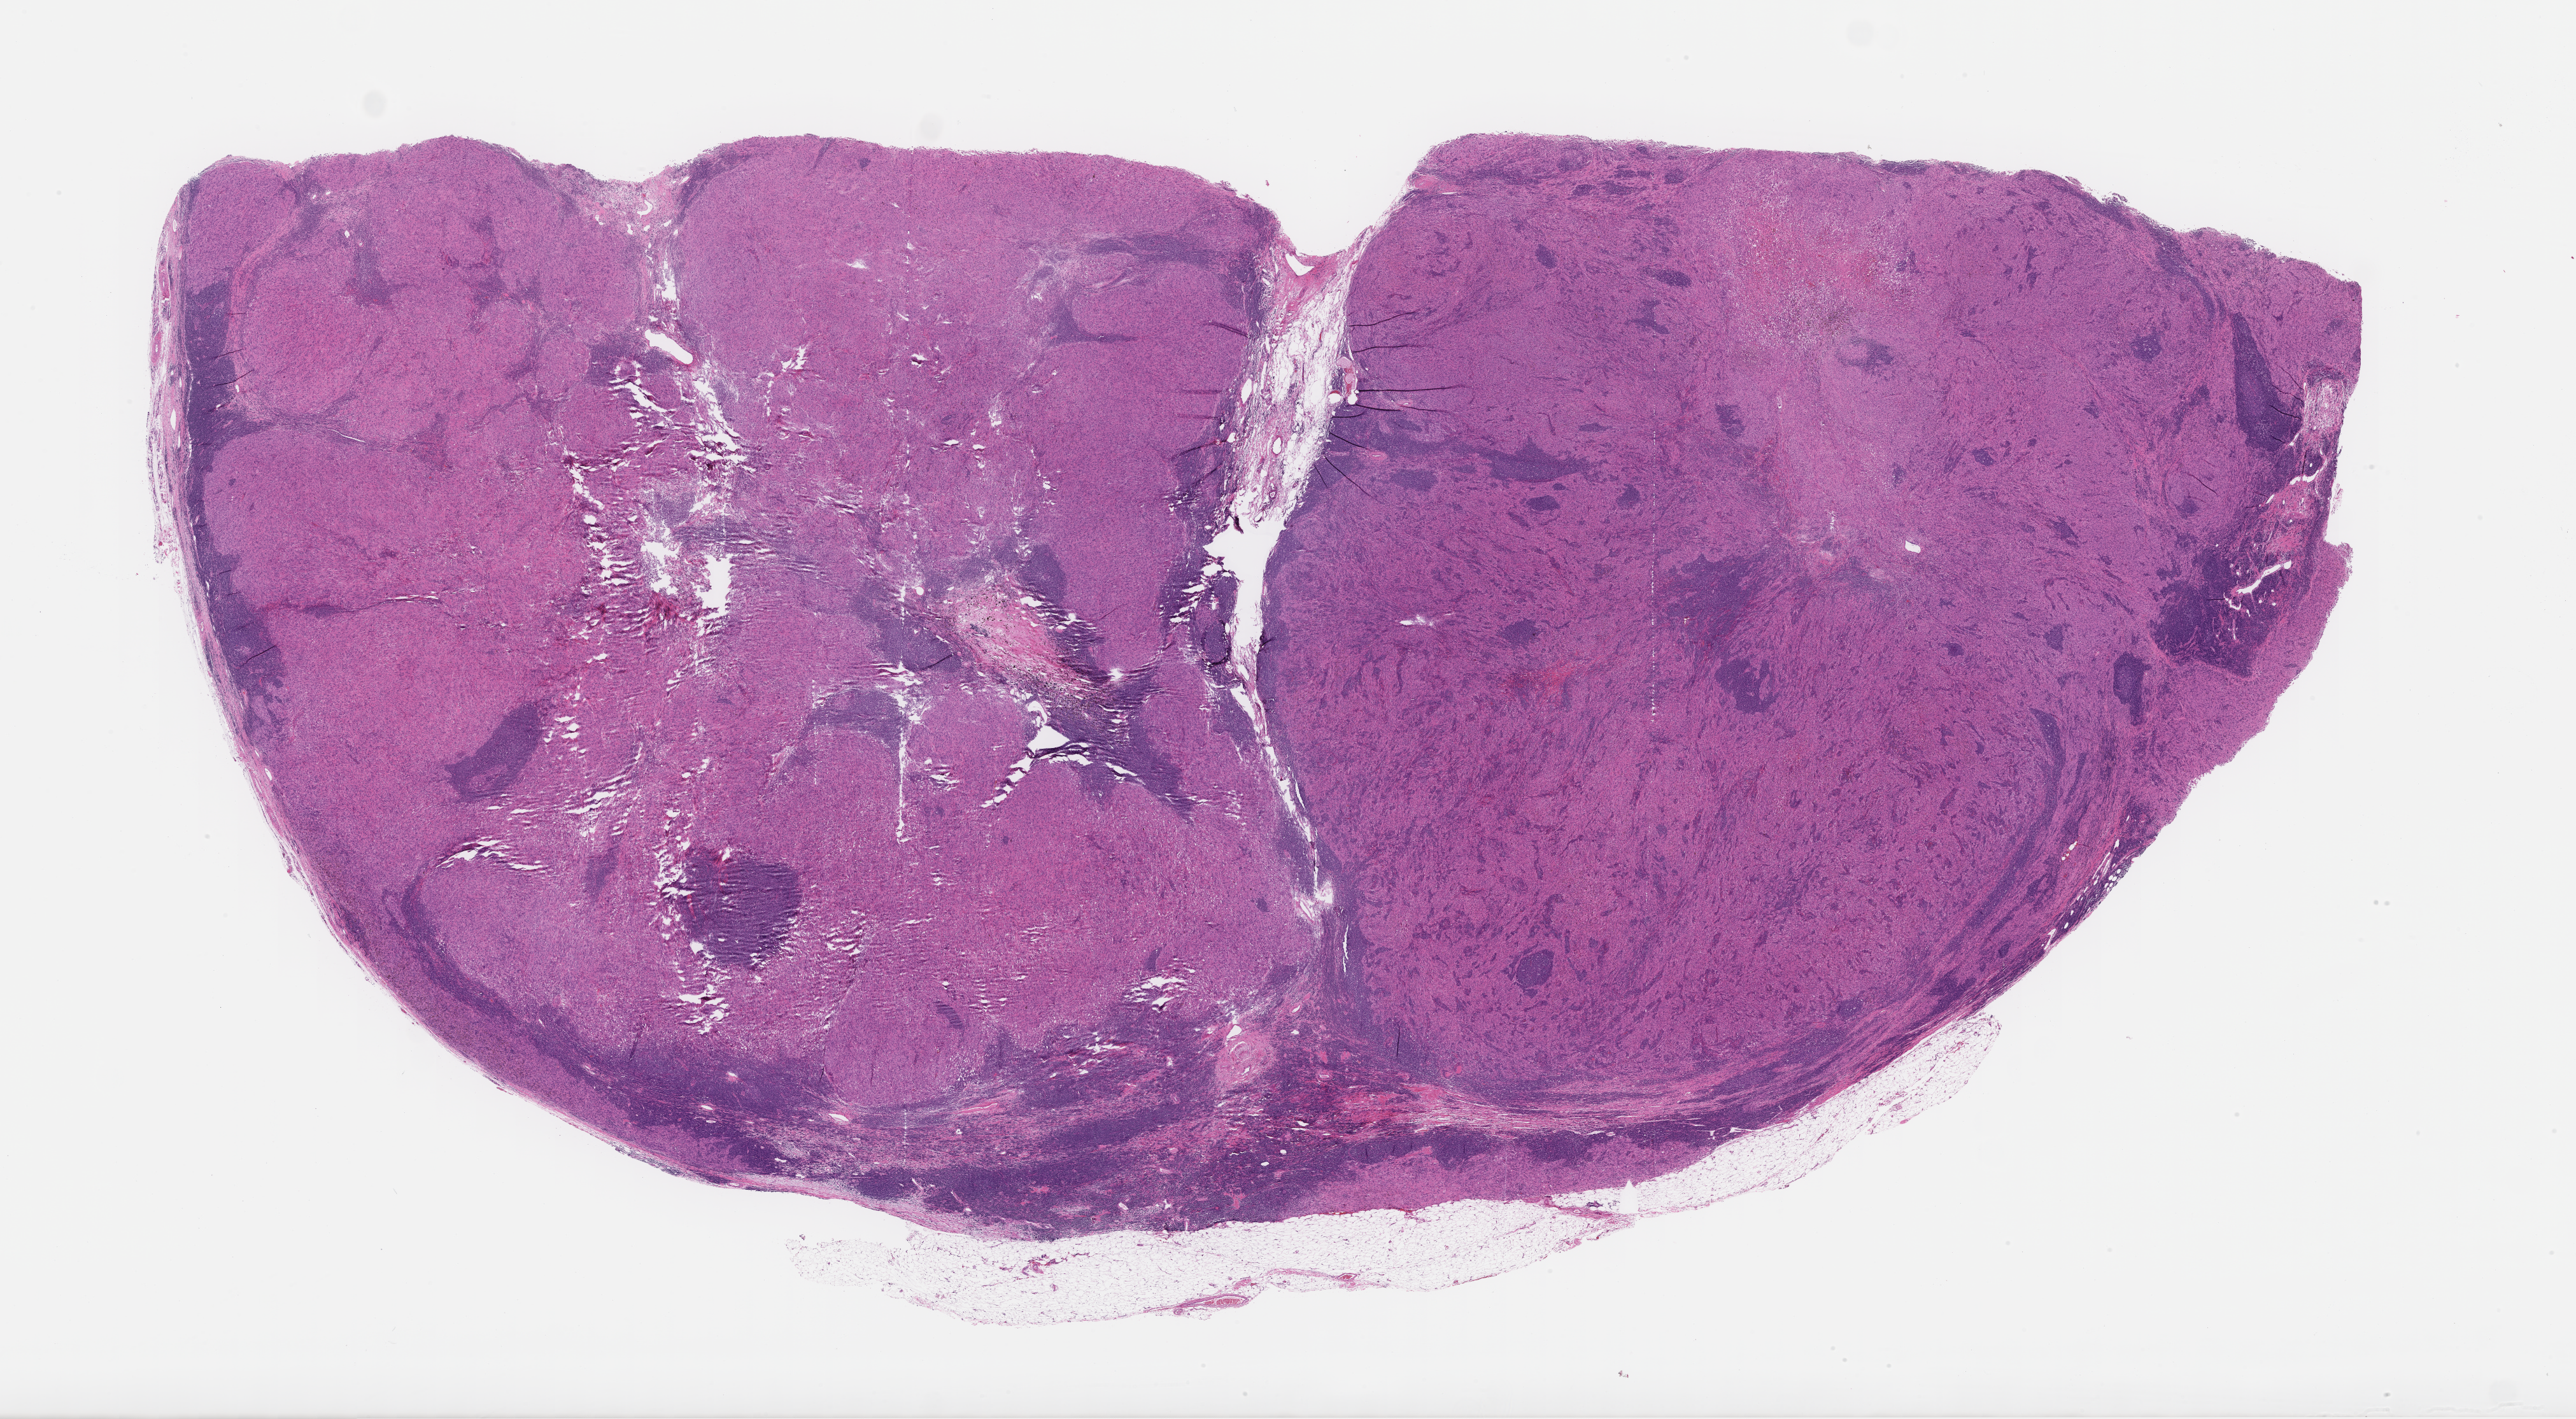
Whole-slide image, hematoxylin and eosin (H&E) stain — shown as a low-resolution overview of the whole scanned area (about 32.7 x 18.0 mm). FFPE section. Patient sex: female.
• this section: metastasis (sampled organ not recorded)
• patient diagnosis (primary): Melanoma